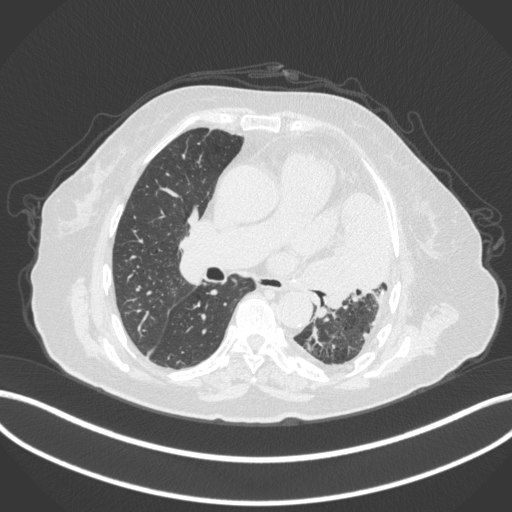
Chest CT, one axial slice; position 202 of 399 along the scan axis; reconstruction kernel B31f; lung window (W 1500 / L -600 HU); 512 × 512 image matrix, field of view 400 × 400 mm. Patient: female, 75 years. From the clinical record (not read from this slice): clinical TNM (as recorded): T3 N3 M1.
Annotated regions visible in this slice (bounding box drawn by a radiologist):
- lung tumour (recorded histology: adenocarcinoma): bounding box <305,185,394,307> (left, top, right, bottom; pixels)